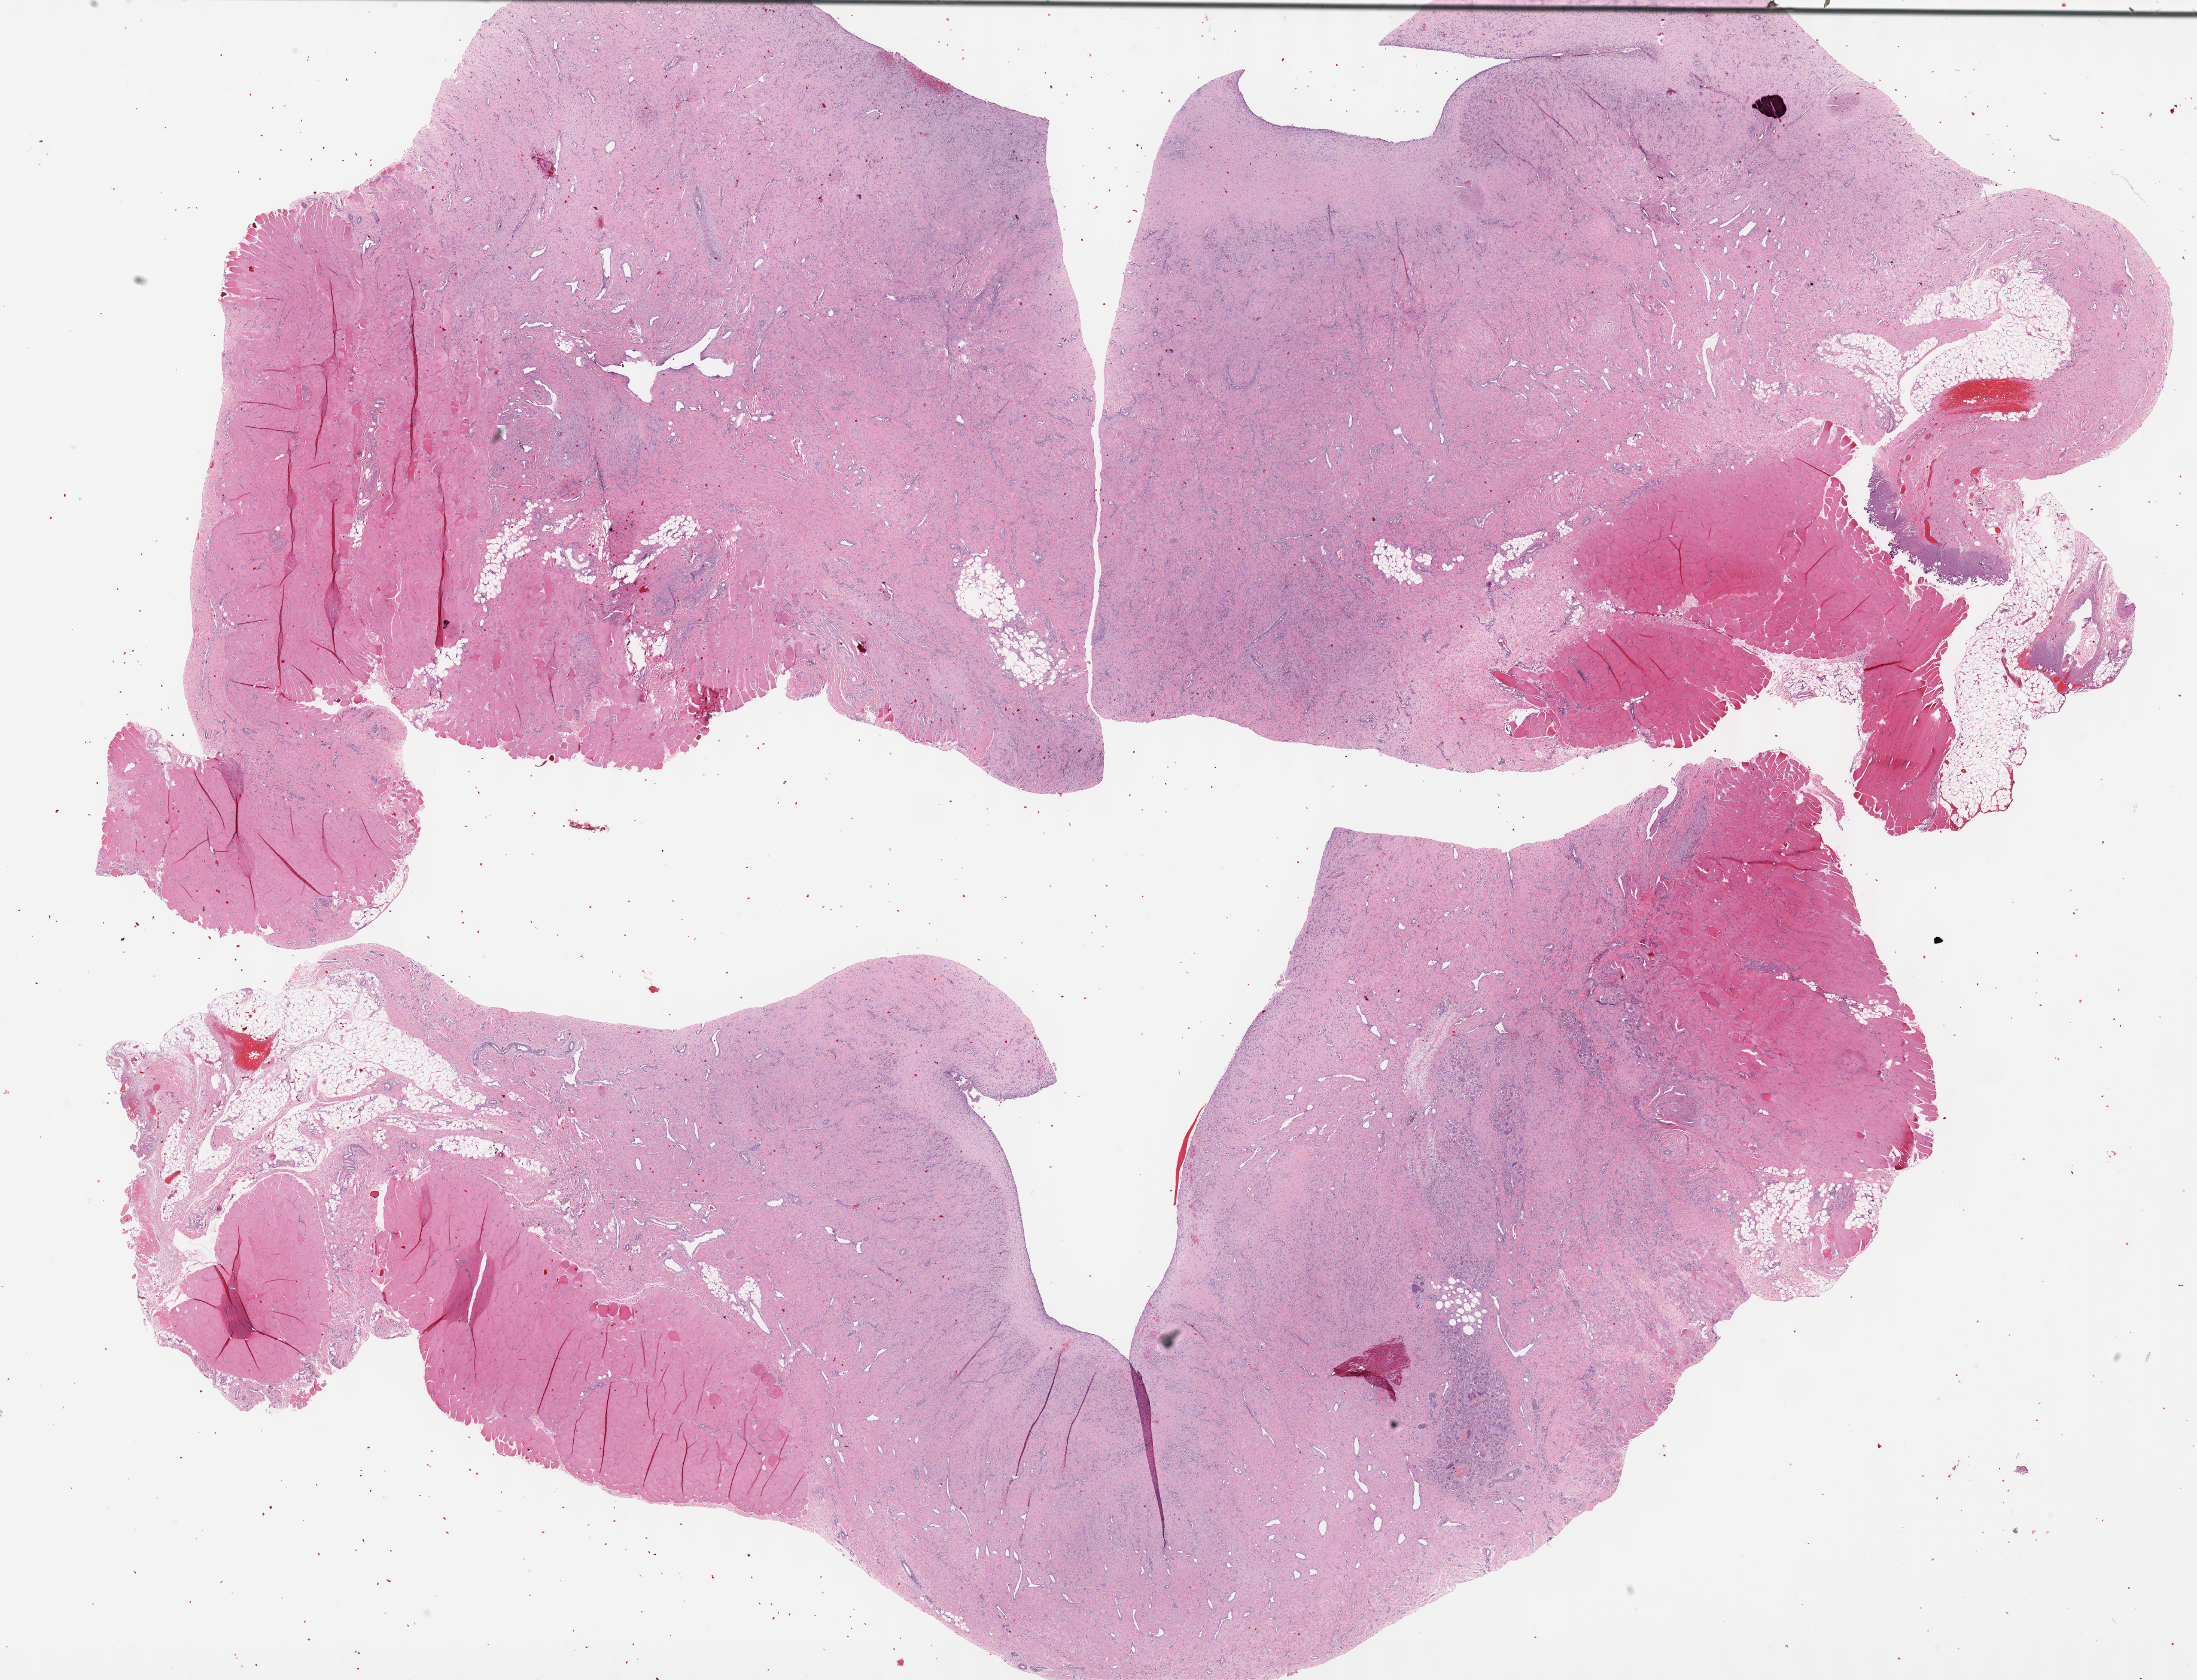
Digitized H&E tissue section (whole slide), whole scanned area (about 29.7 x 22.7 mm) shown as a low-resolution overview. Formalin-fixed paraffin-embedded (FFPE) diagnostic section. Primary tumour sample from the connective, subcutaneous and other soft tissues. Patient: male, age at initial diagnosis 35 years.
- diagnosis: Fibromyxosarcoma